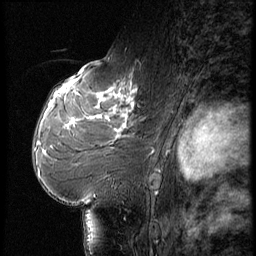
Breast MRI (dynamic contrast-enhanced), one sagittal slice; position 36 of 56 along the scan axis; dynamic contrast-enhanced series, image 2 of 3 at this slice position (ordered by acquisition); 1.5 T; TE 4.2 ms, TR 9 ms; 2.5 mm slice thickness; 256 × 256 image matrix, field of view 180 × 180 mm. Female patient, age 61 years. Case-level facts recorded for this patient, not image findings: setting: breast cancer imaged before/during neoadjuvant chemotherapy; receptor status: HR-positive, HER2-negative.
Outlined on this slice (semi-automatically segmented with operator editing):
- analysis volume of interest (the breast-tissue region the enhancement analysis was run in; not a lesion): box from (x=65, y=74) to (x=149, y=175) px
- tumour enhancement mask (voxels above the 140 % enhancement threshold inside the analysis volume of interest): (x=68, y=89)–(x=137, y=128)